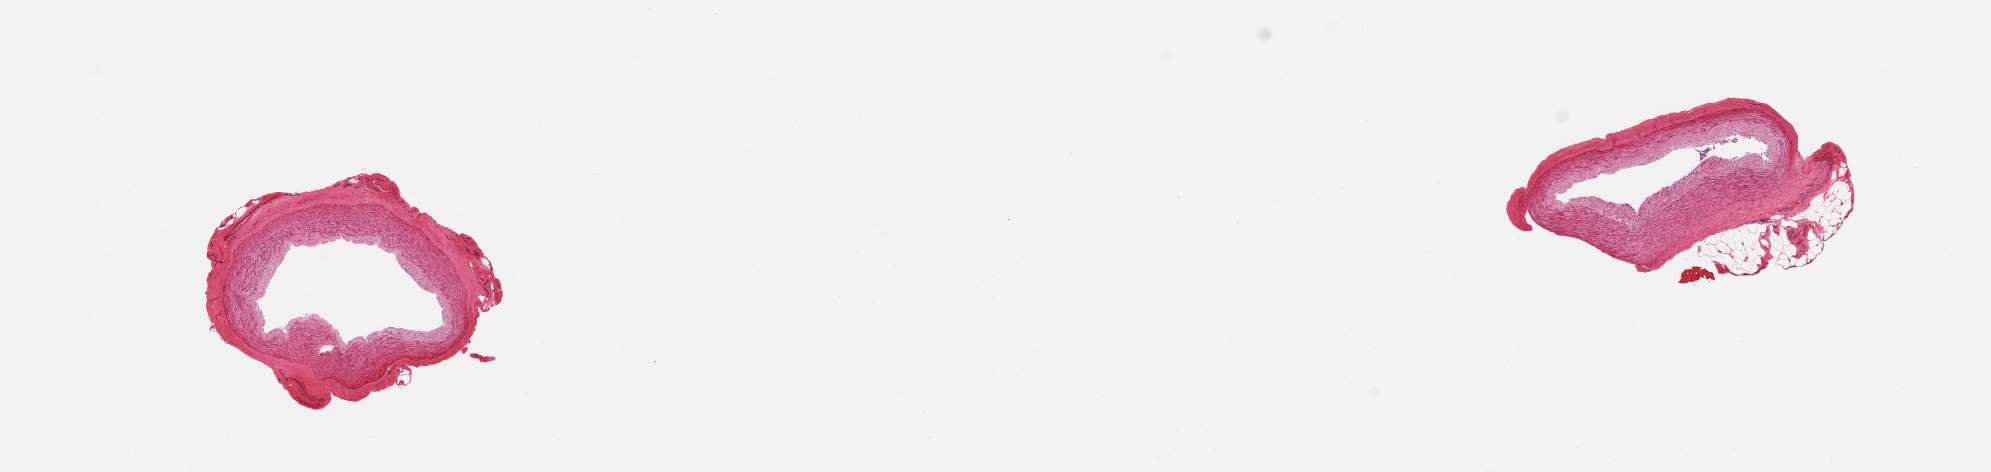
Whole-slide image, H&E stain — low-resolution overview of the scanned area, about 15.8 x 3.7 mm; PAXgene-fixed, paraffin-embedded tissue; target tissue: tibial artery; tissue donor sample. Male donor.
Reviewer comment on this tissue sample: 2 pieces; slight intimal thickening; no plaque; 1 mm external fat deposit on 1 piece.